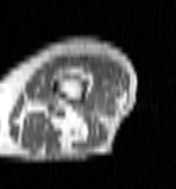
MRI of an extremity soft-tissue mass, one axial slice; position 25 of 100 along the scan axis; MR volume resampled by the dataset authors to the PET/CT grid (not the native acquisition matrix); 3.27 mm slice thickness; 176 × 189 image matrix, field of view 172 × 185 mm. Female patient. From the clinical record (not read from this slice): histological type: undifferentiated – high grade; grade: high; site of the primary tumour: left thigh.
Outlined on this slice (expert contour drawn on MRI and transferred to this co-registered scan by the dataset authors):
- gross tumour volume including surrounding oedema: bounding box (x1, y1, x2, y2) in pixels: (73, 61, 116, 104)